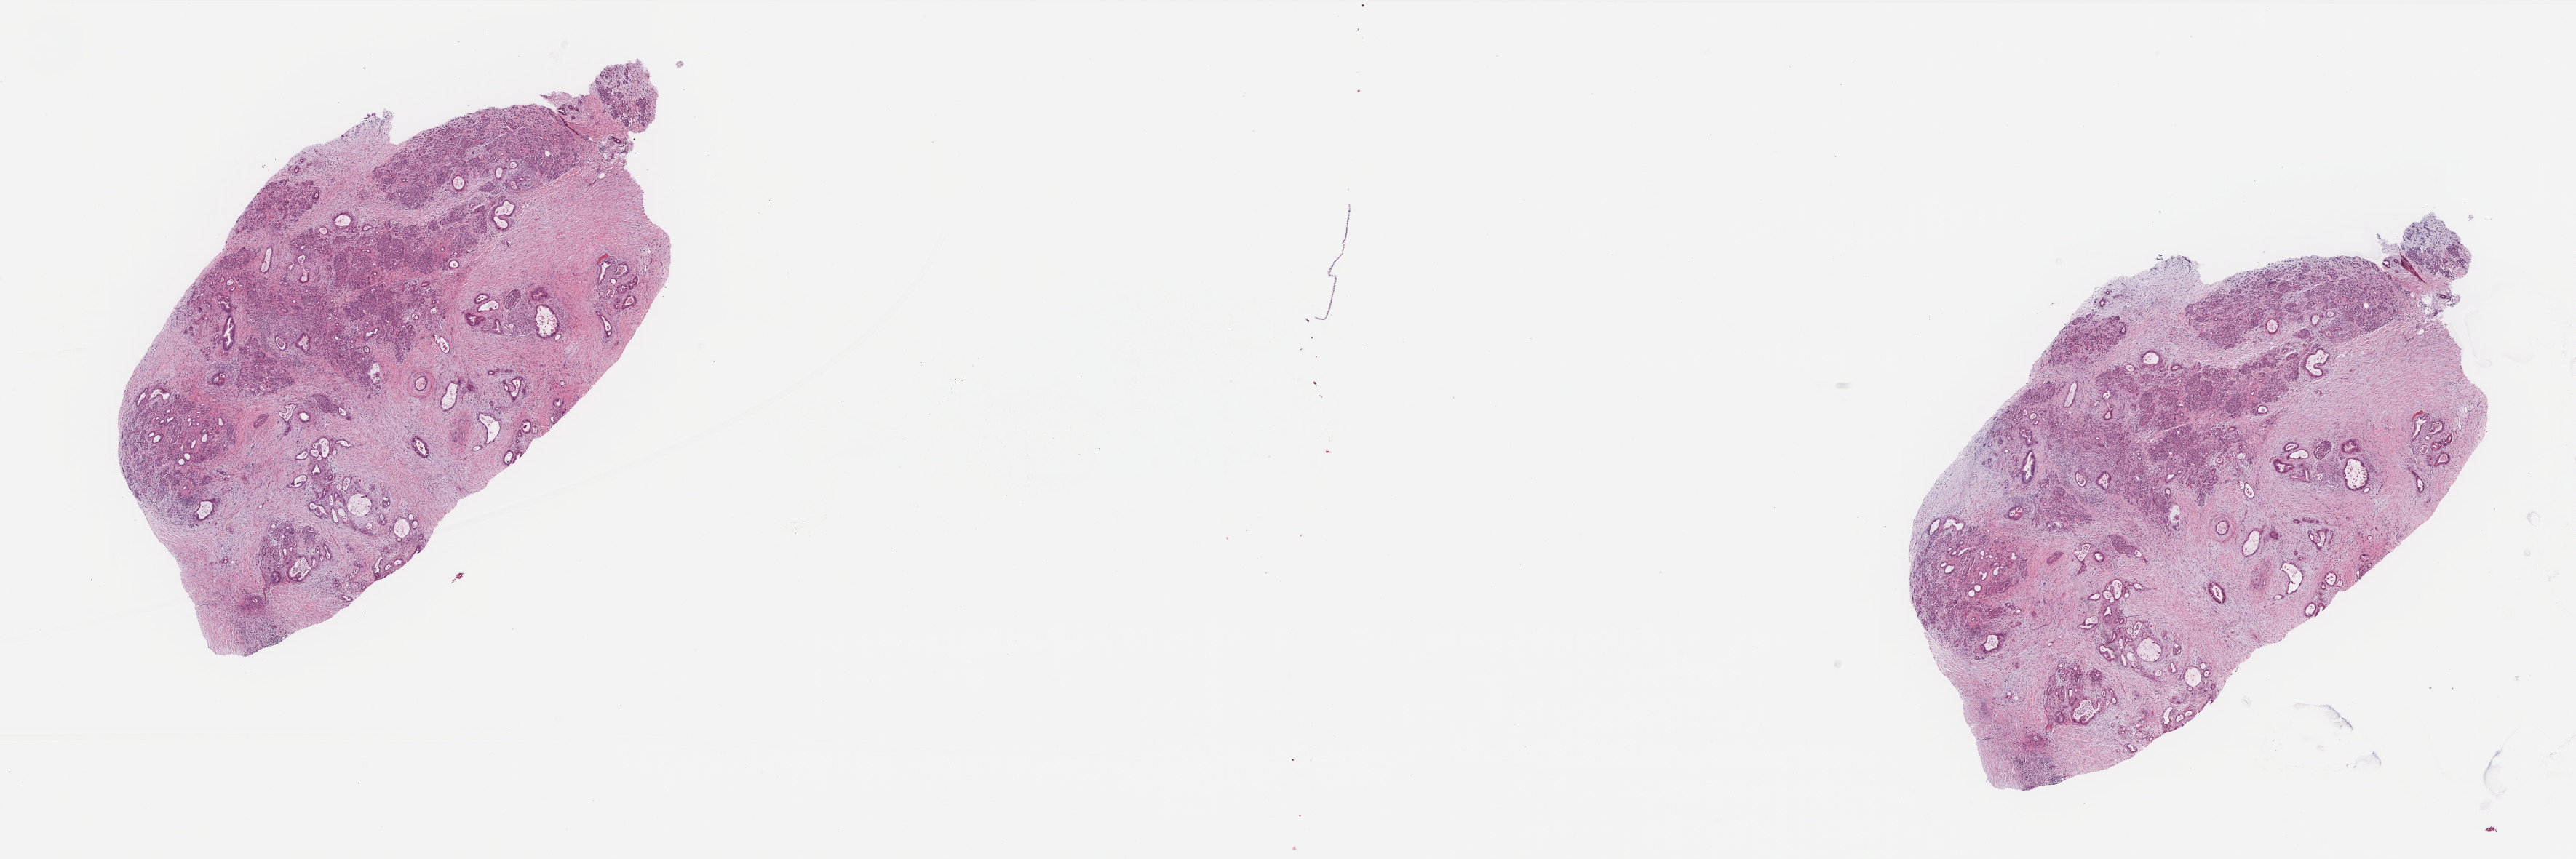
Whole-slide histology image, H&E-stained, low-resolution overview of the scanned area, about 28.4 x 9.5 mm (slide scanned at 40x); FFPE section; primary tumour sample from the pancreas. Female patient. Histologic grade: G3 (poorly differentiated).
* pathologic diagnosis: Adenocarcinoma, NOS
* AJCC pathologic stage: IIB (7th edition)
* lymph nodes positive (case pathology): 1 of 12 examined